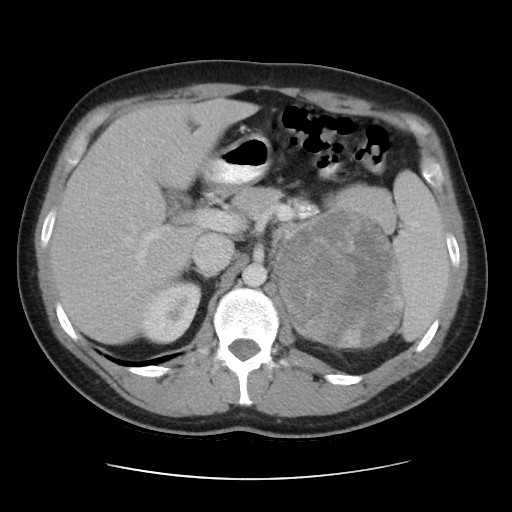
Contrast-enhanced abdominal CT, one axial slice. Slice 28 of 48 in the series (ordered by position). Reconstruction kernel STANDARD. 120 kVp. Intravenous contrast given. Soft-tissue window (W 400 / L 40 HU). 5 mm slice thickness. 512 × 512 image matrix, field of view 360 × 360 mm. Male patient, age 32 years. Case-level facts recorded for this patient, not image findings: diagnosis: adrenocortical carcinoma; tumour side: left adrenal; tumour size at pathology: 14 cm; Ki-67 index: 67 %; stage (as recorded): 3.
Annotated regions visible in this slice (semi-automatic segmentation, software-assisted and operator-edited):
- mass: bounding box [x1, y1, x2, y2] px = [280, 214, 399, 345]